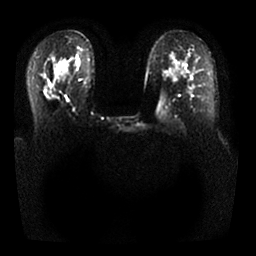
Breast MRI, one axial slice. Slice 17 of 25 in the series (ordered by position). Diffusion-weighted series; image 2 of 4 stored at this slice position (different b-values; order by instance number). 1.5 T. 4 mm slice thickness. 256 × 256 image matrix. Female patient.
Structures marked on this image (outlined manually by an expert reader):
- tumour on diffusion-weighted imaging: bounding box (x1, y1, x2, y2) in pixels: (45, 93, 51, 98)